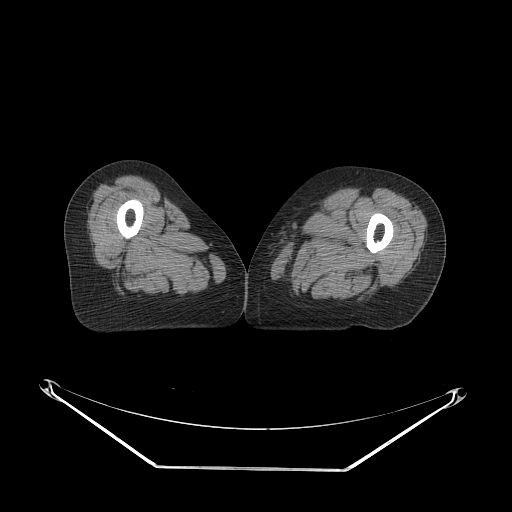
CT of an extremity soft-tissue mass (from a PET/CT study), one axial slice. Slice 54 of 91 in the series (ordered by position). Reconstruction kernel STANDARD. 140 kVp. Soft-tissue window (W 400 / L 40 HU). 3.75 mm slice thickness. 512 × 512 image matrix, field of view 500 × 500 mm. Female patient. Case-level facts recorded for this patient, not image findings: histological type: pleomorphic leiomyosarcoma; grade: high; site of the primary tumour: left thigh.
Outlined on this slice (expert contour drawn on MRI and transferred to this co-registered scan by the dataset authors):
- gross tumour volume including surrounding oedema: bounding box (x1, y1, x2, y2) in pixels: (276, 203, 311, 227)